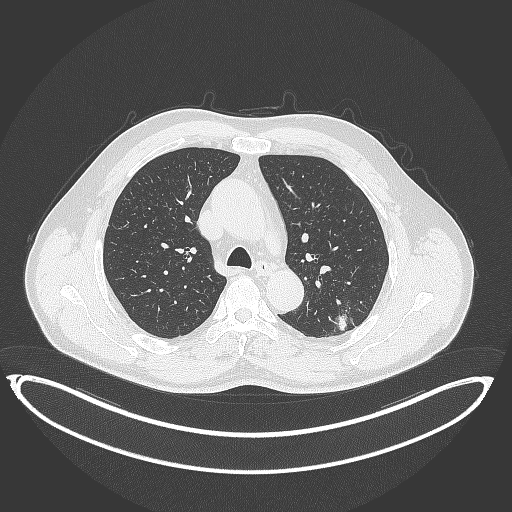
Chest CT, one axial slice; 120 kVp; lung window (W 1500 / L -600 HU); 1 mm slice thickness; 512 × 512 image matrix, field of view 469 × 469 mm. Patient: male, 58 years. Case-level facts recorded for this patient, not image findings: clinical TNM (as recorded): T1c N0 M0.
Structures marked on this image (rectangle marked by the reading radiologist):
- lung tumour (recorded histology: adenocarcinoma): box from (x=326, y=307) to (x=356, y=338) px